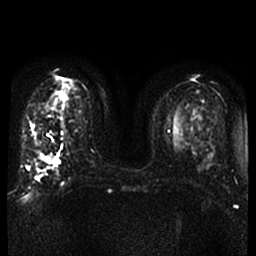
Breast MRI, one axial slice; diffusion-weighted series; image 2 of 4 stored at this slice position (different b-values; order by instance number); 1.5 T; 256 × 256 image matrix. Female patient.
Outlined on this slice (expert manual segmentation):
- tumour on diffusion-weighted imaging: bounding box <41,155,54,164> (left, top, right, bottom; pixels)